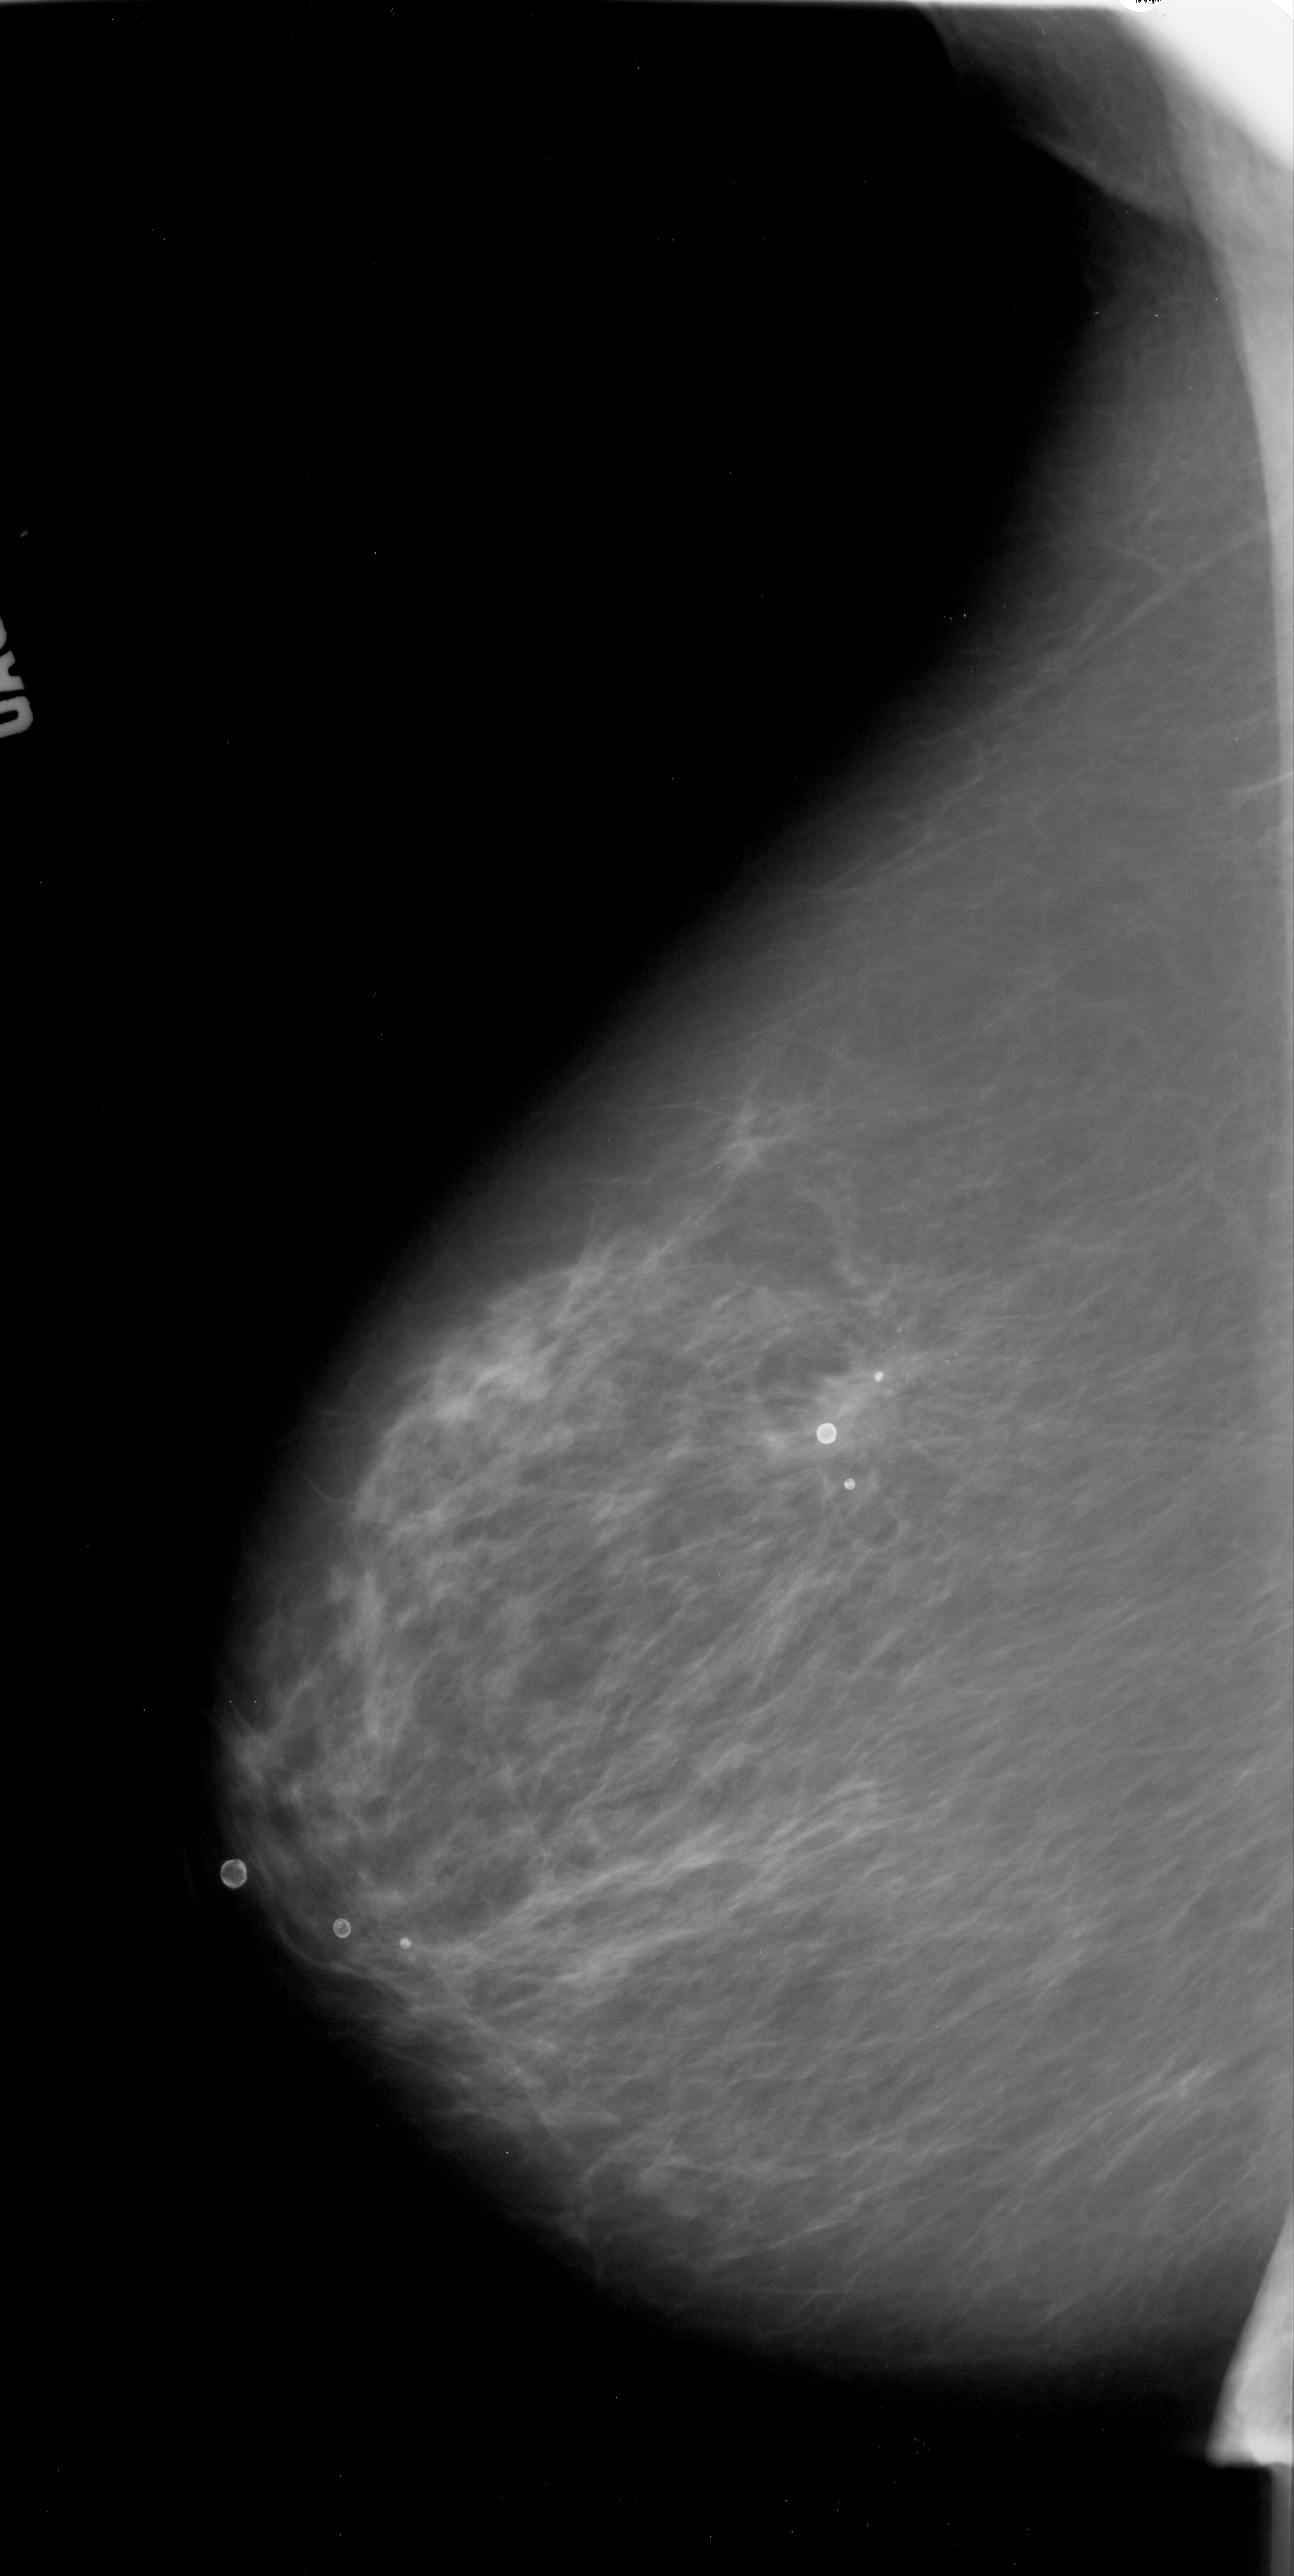
Mammogram (digitized film), left breast, mediolateral oblique (MLO) view, breast composition: scattered fibroglandular densities (BI-RADS density category 2 of 4).
- Calcifications, morphology pleomorphic, distribution linear; BI-RADS assessment category 4; pathology (as recorded): malignant.